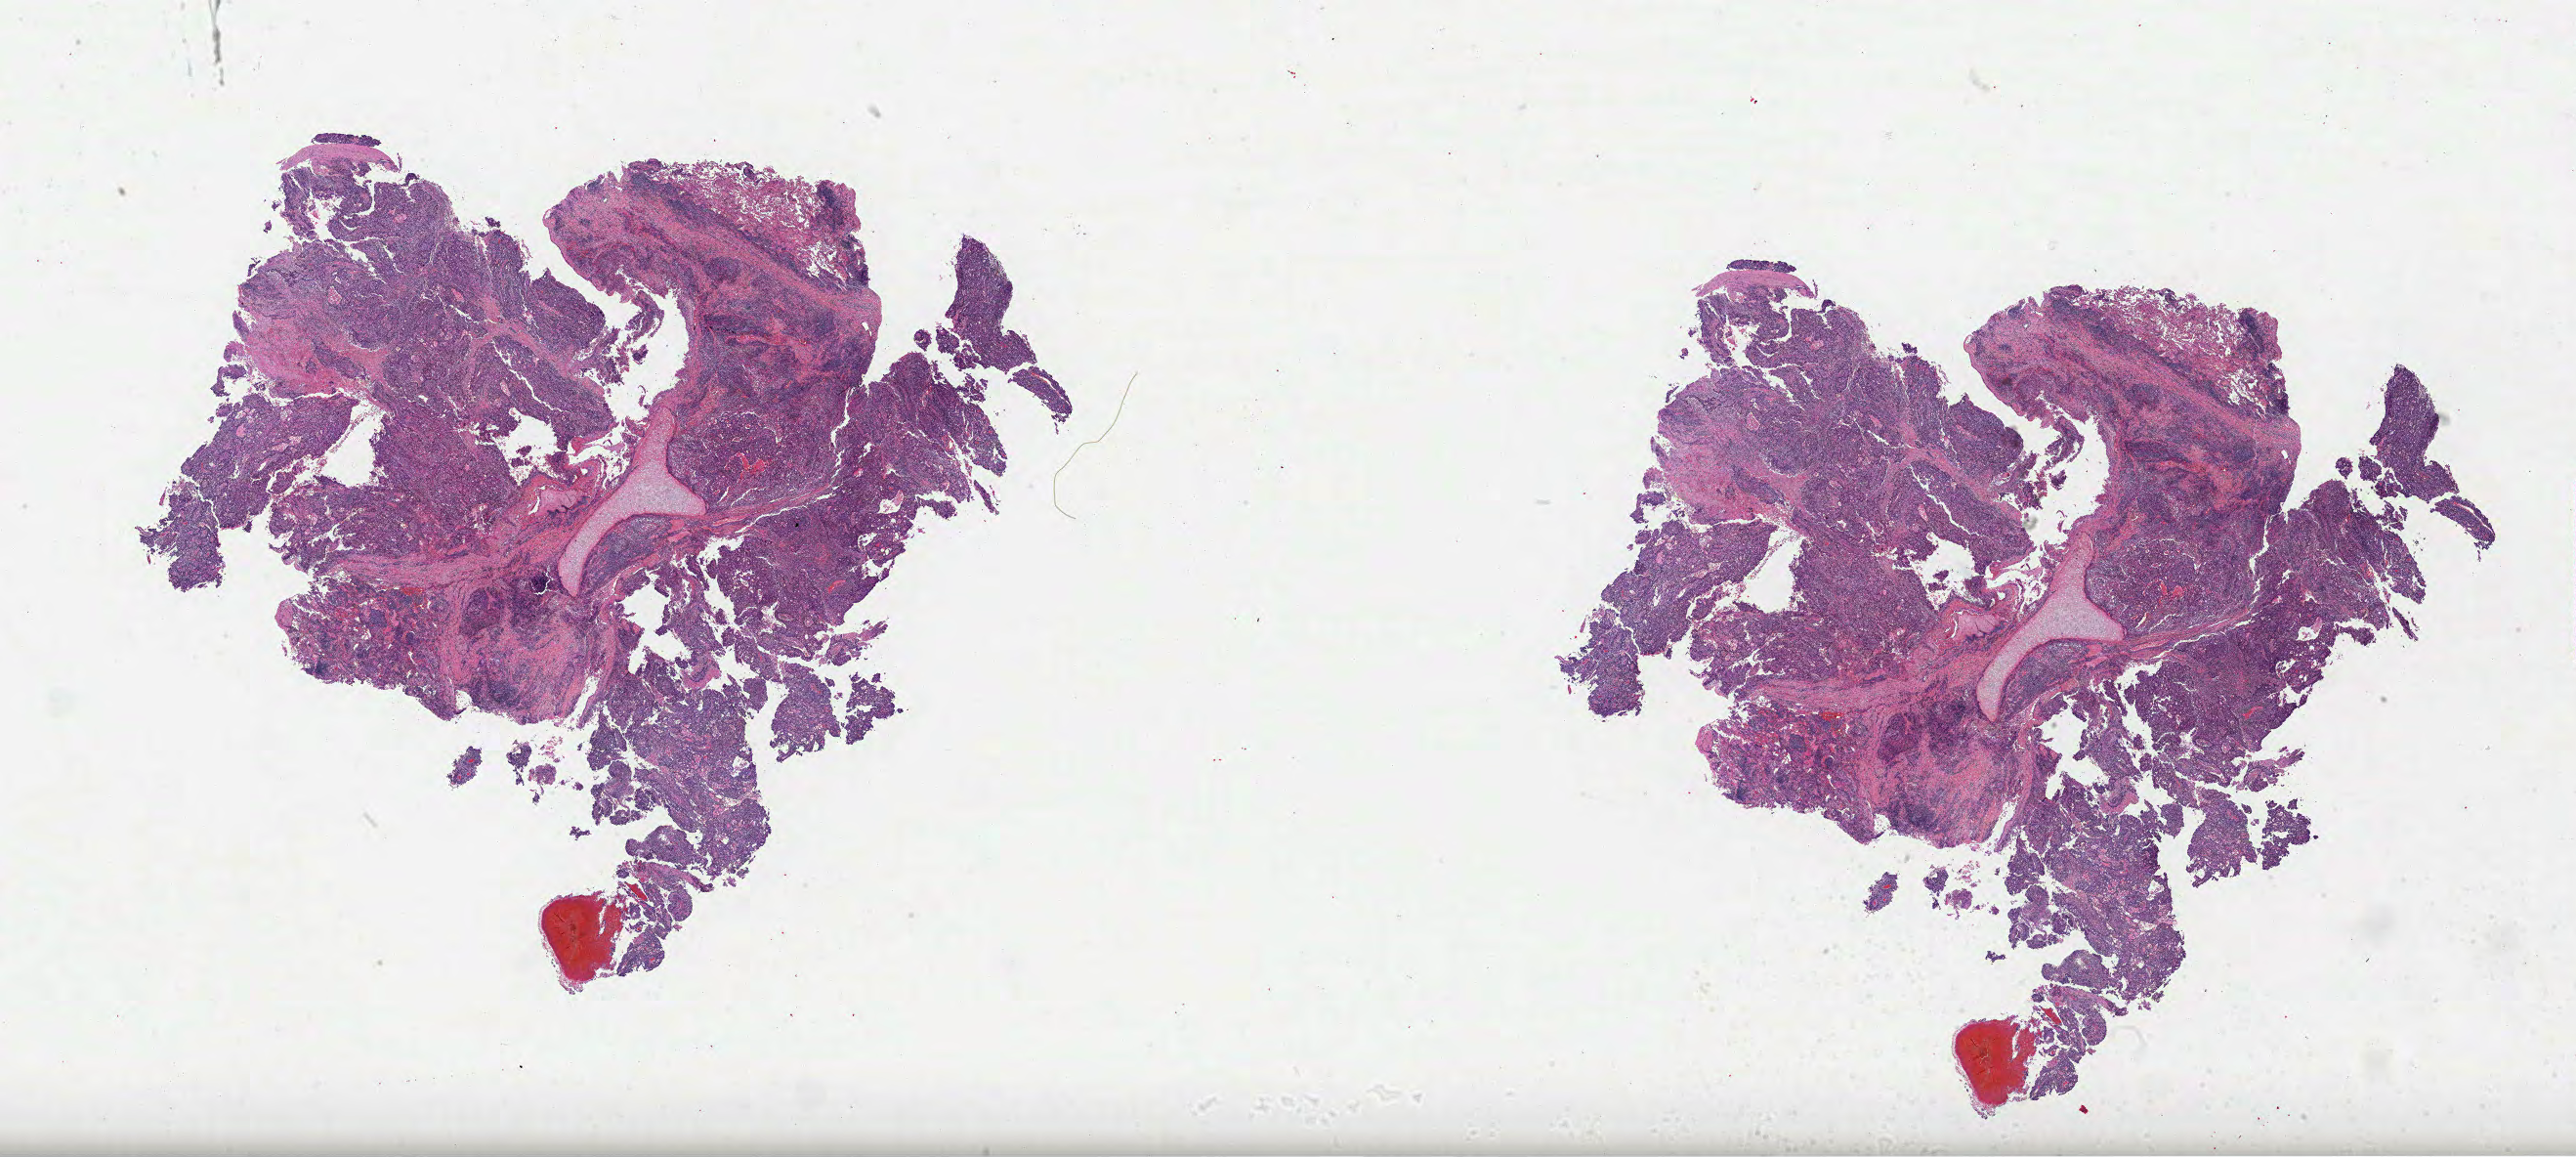
Hematoxylin and eosin (H&E) stained whole-slide image — low-resolution overview of the scanned area, about 42.5 x 19.1 mm (slide scanned at 40x), FFPE section, sample: primary tumour, lung. Patient: male, age at initial diagnosis 56 years.
Laterality: right. Histologic diagnosis: Squamous cell carcinoma, NOS (upper lobe, lung). AJCC pathologic stage: IA (7th edition). TNM: T1b N0 M0.